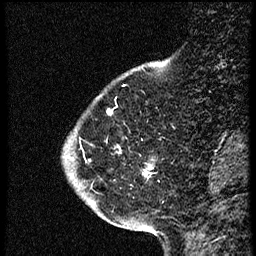
Breast MRI (dynamic contrast-enhanced), one sagittal slice. Dynamic contrast-enhanced study with each time point stored as its own series, time point 2 of 4 at this slice position (early post-contrast, ordered by acquisition time). 1.5 T. TE 4.2 ms, TR 18.9 ms. 256 × 256 image matrix, field of view 200 × 200 mm. Female patient. From the clinical record (not read from this slice): setting: breast cancer imaged before/during neoadjuvant chemotherapy; receptor status: HER2-positive.
Structures marked on this image (semi-automatically segmented with operator editing):
- analysis volume of interest (the breast-tissue region the enhancement analysis was run in; not a lesion): bounding box [x1, y1, x2, y2] px = [64, 94, 154, 215]
- tumour enhancement mask (voxels above the 100 % enhancement threshold inside the analysis volume of interest): [109, 112, 148, 175]